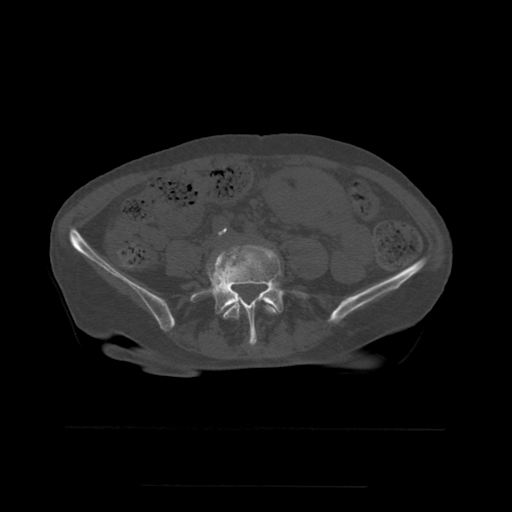
CT including the spine, one axial slice. Position 153 of 544 along the scan axis. Bone window (W 1800 / L 400 HU). 1.25 mm slice thickness. 512 × 512 image matrix. Patient age 58 years. From the clinical record (not read from this slice): primary cancer: lung.
Structures marked on this image (semi-automatically segmented with operator editing):
- L4 vertebra: box from (x=210, y=251) to (x=277, y=320) px
- L5 vertebra: (x=191, y=246)–(x=302, y=345)